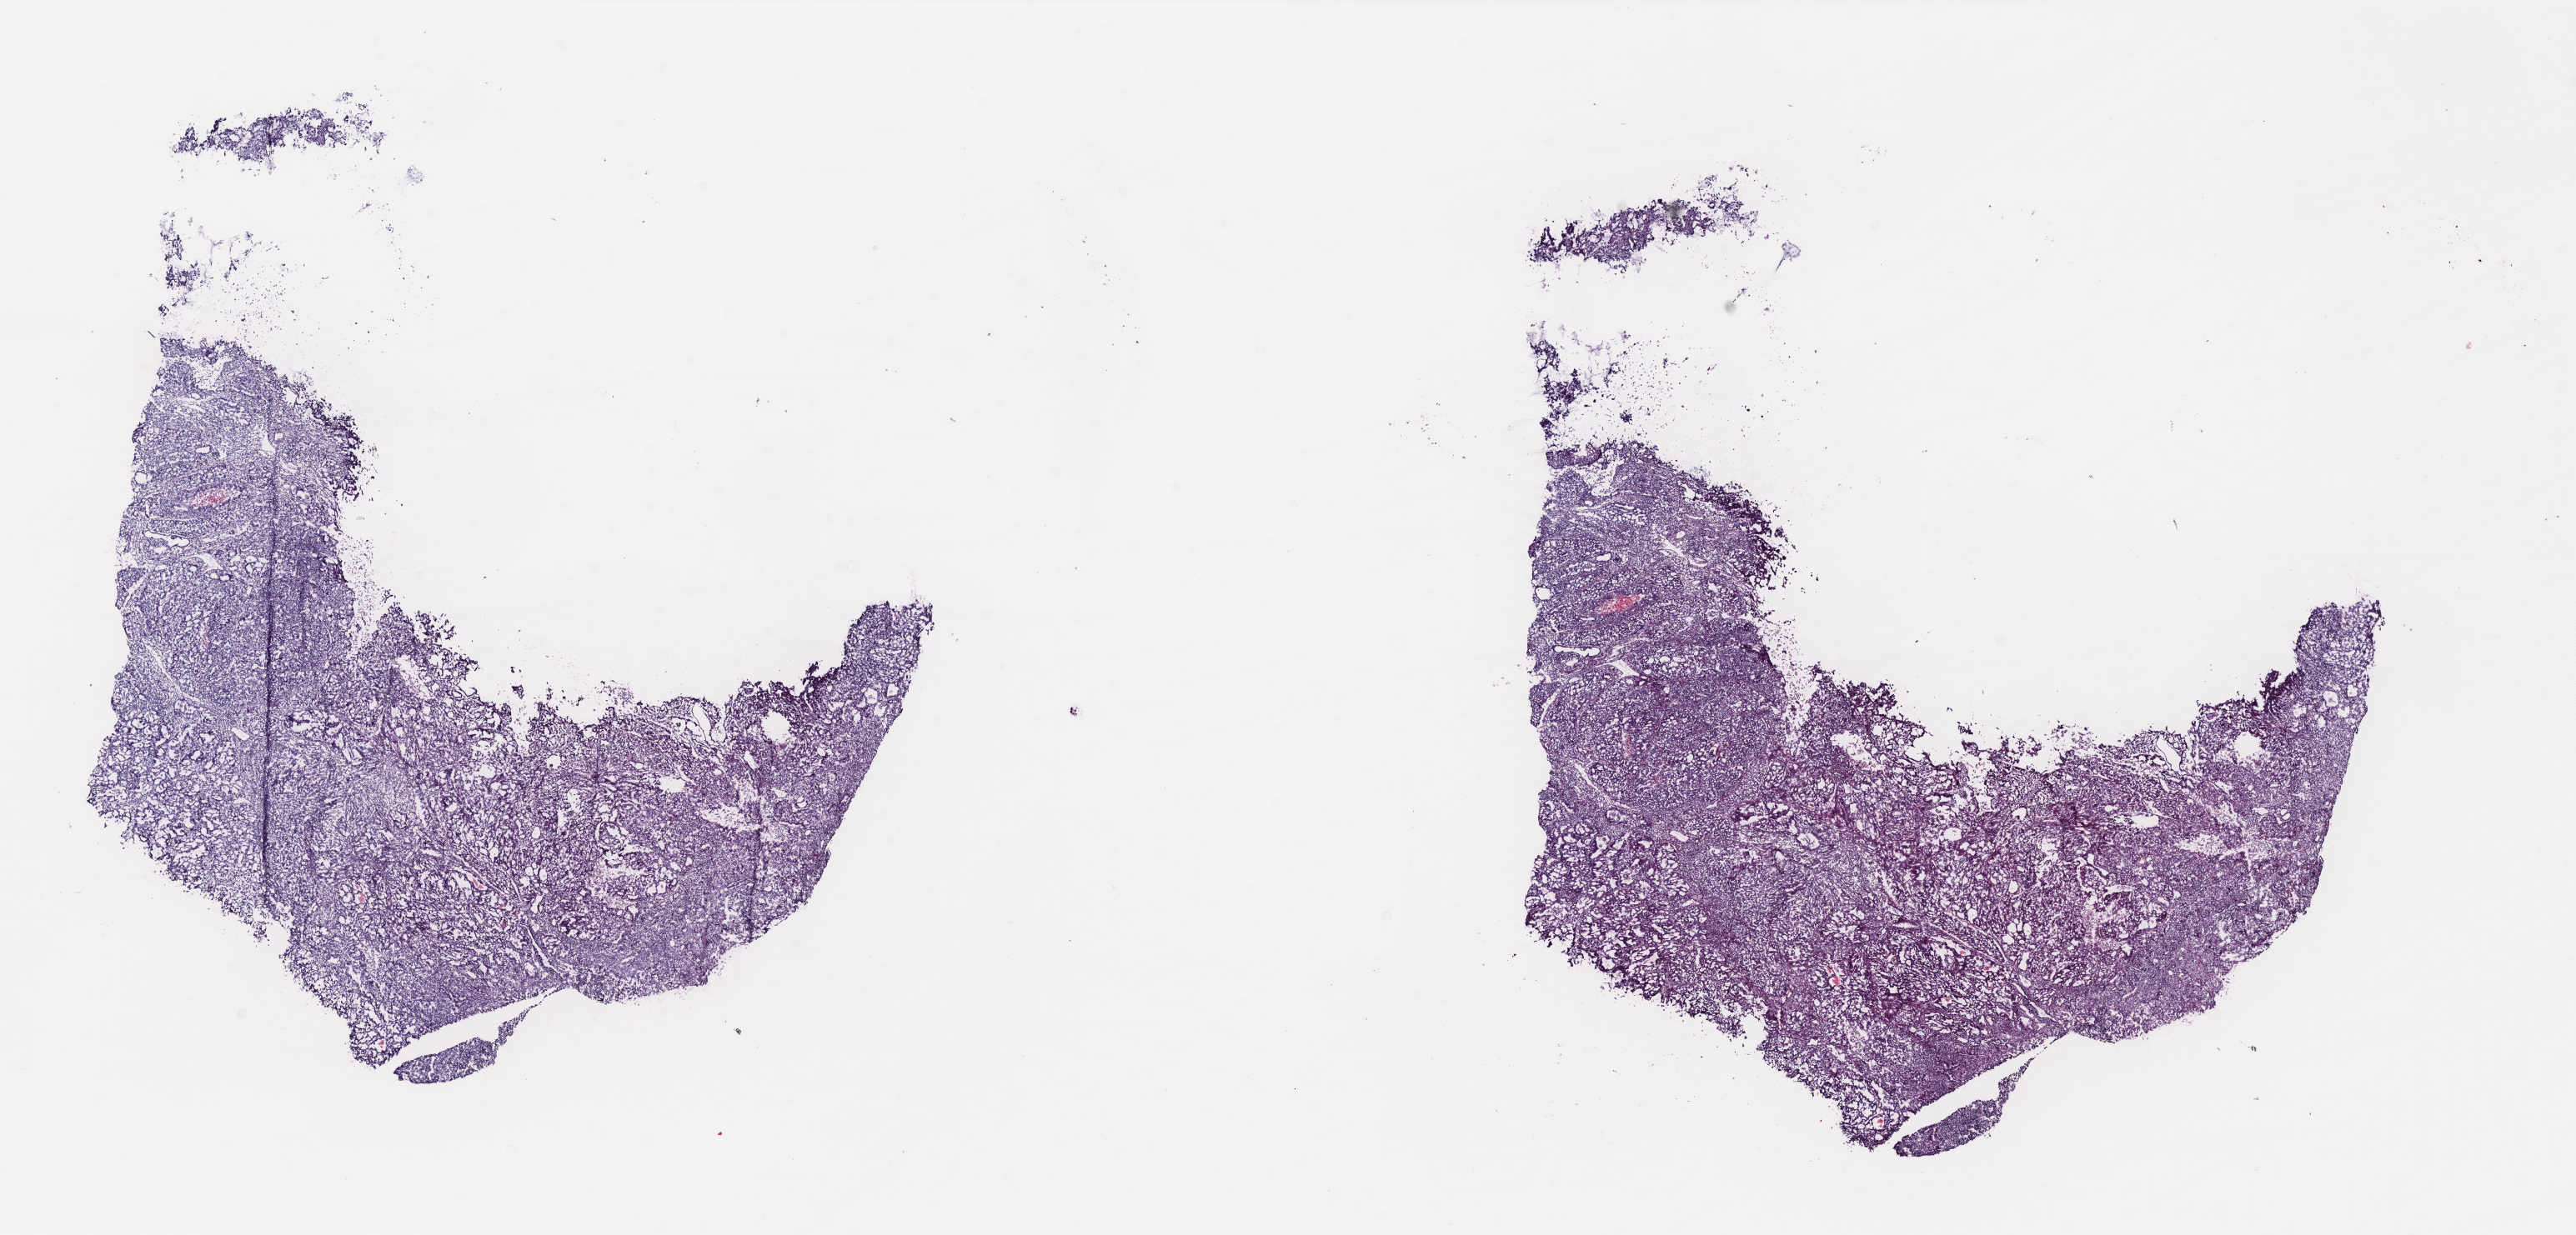
Digitized Hematoxylin and eosin (H&E) stained tissue section (whole slide) — shown as a low-resolution overview of the whole scanned area (about 24.8 x 11.9 mm); frozen section from the bottom of the tissue portion; primary tumour sample from the uterus. Patient: female, age at initial diagnosis 50 years.
Pathologic diagnosis: Endometrioid adenocarcinoma, NOS.